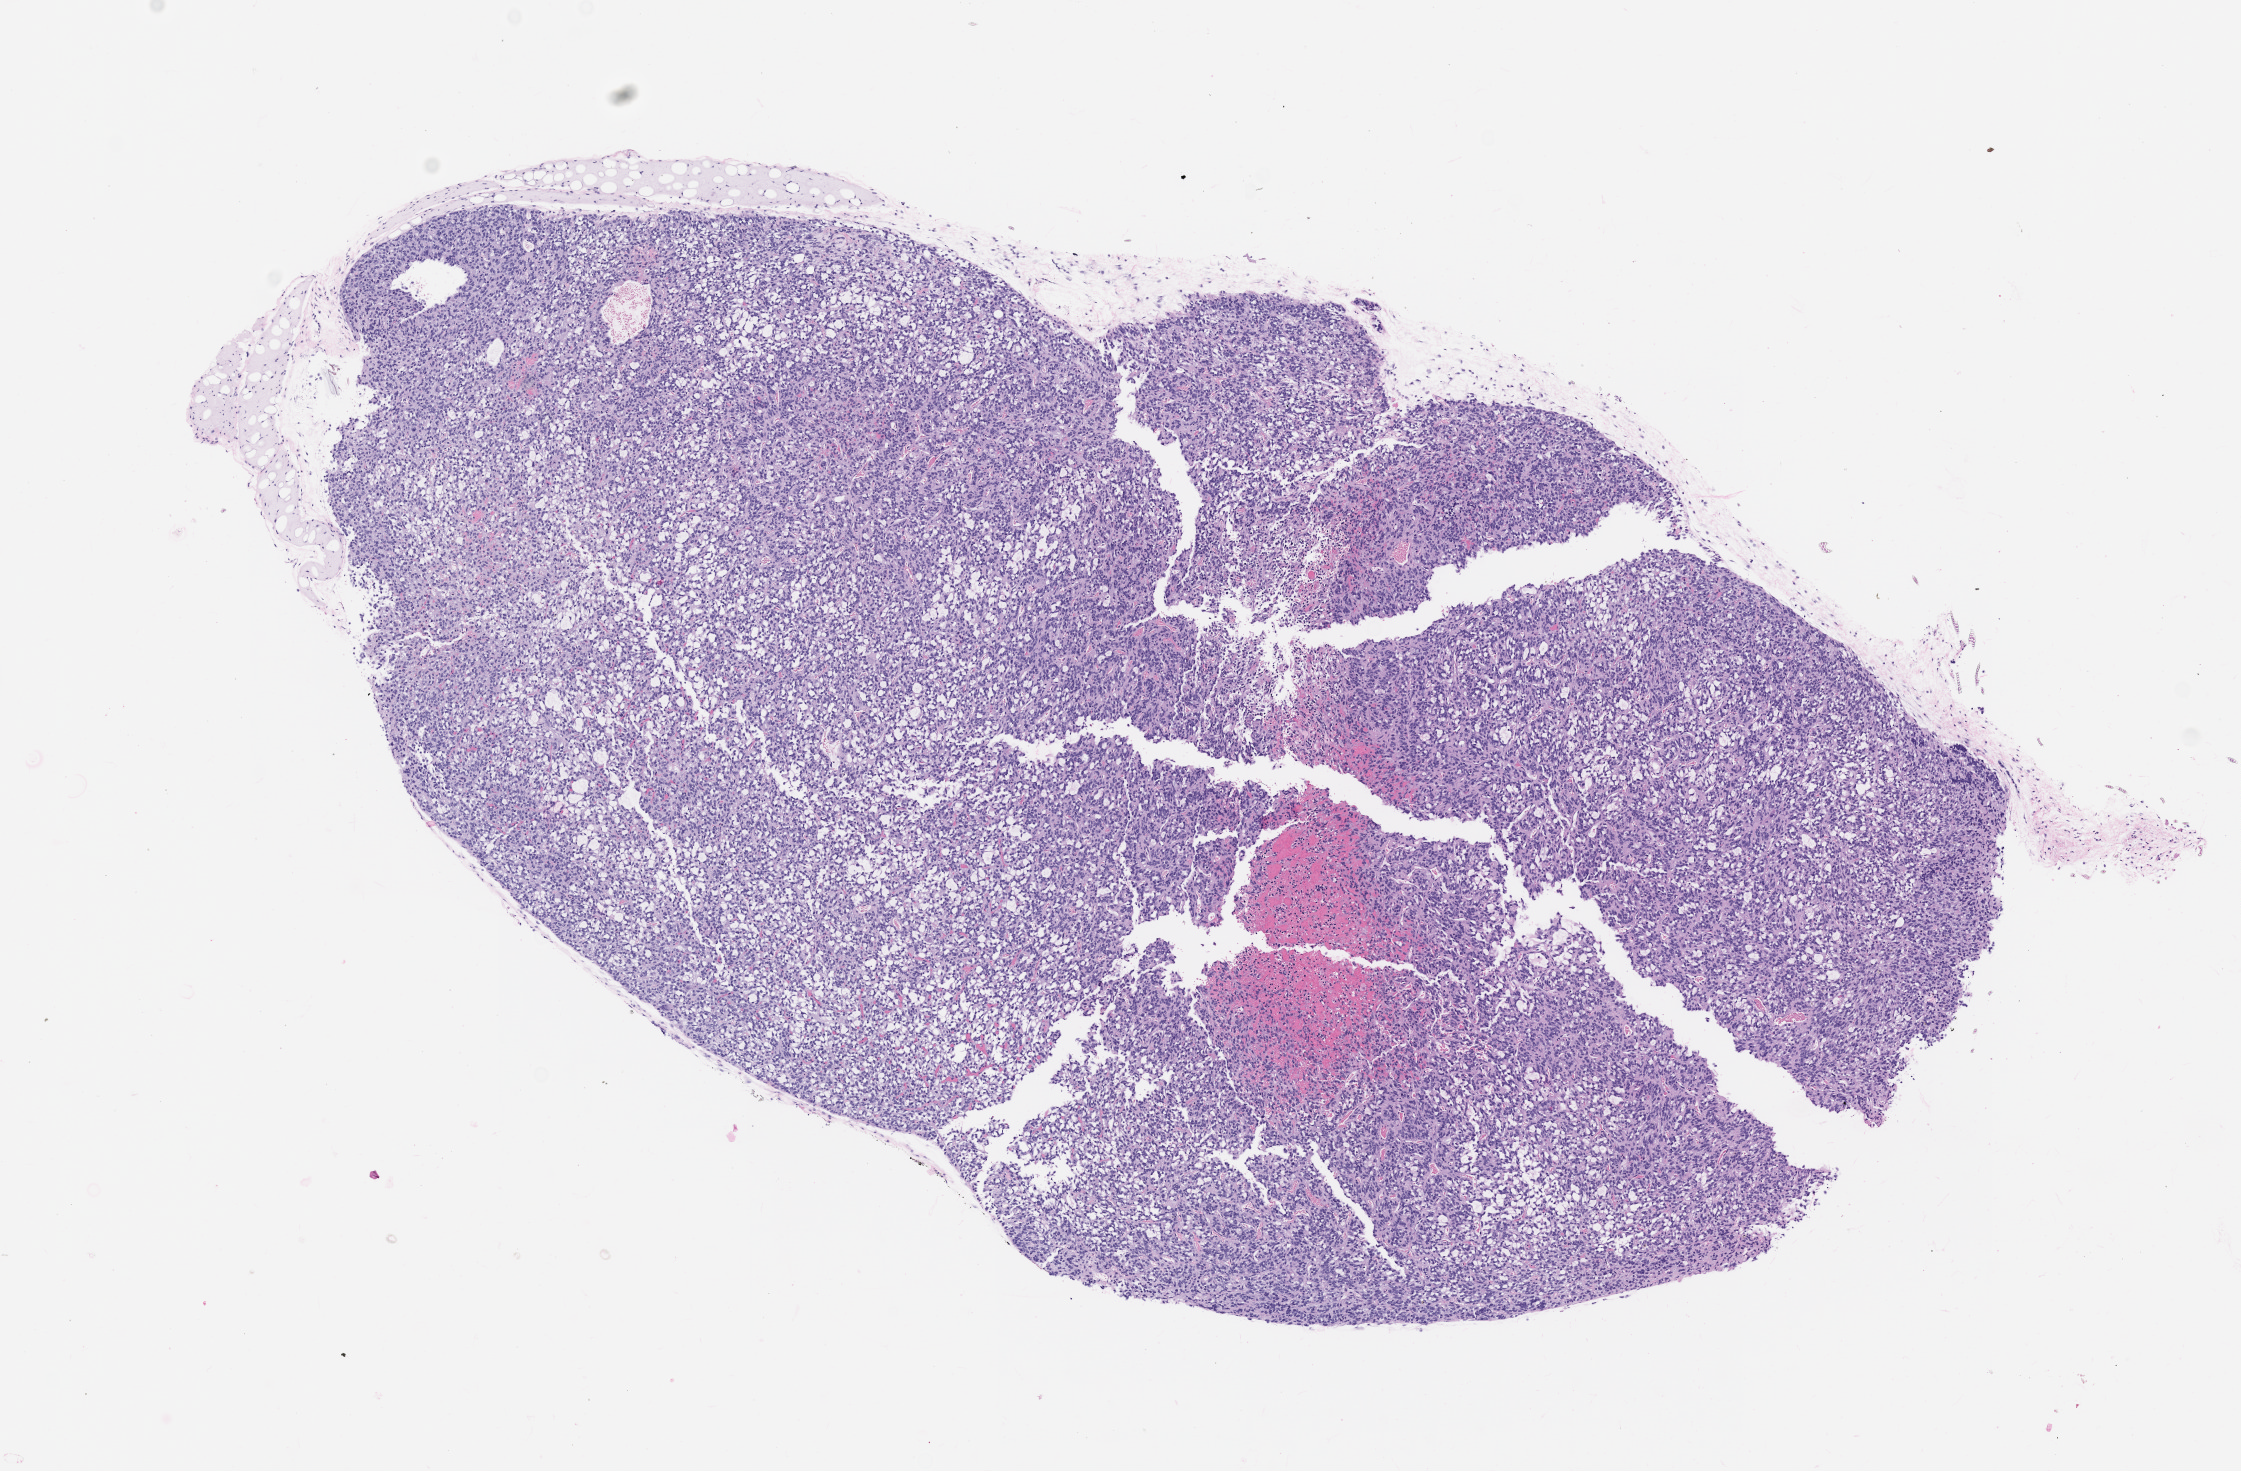
Whole-slide image, hematoxylin and eosin (H&E): patient-derived xenograft (human tumor grown in a mouse), passage 1, shown as a low-resolution overview of the whole scanned area (about 9.0 x 5.9 mm); FFPE section; tumor site category: uterus.
Originating patient diagnosis: Leiomyosarcoma.